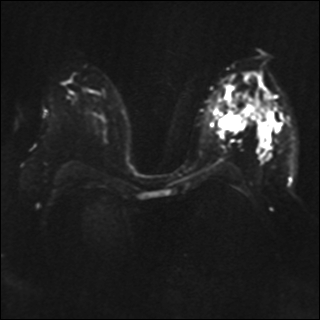
Breast MRI, one axial slice. Position 22 of 41 along the scan axis. Diffusion-weighted series; image 2 of 4 stored at this slice position (different b-values; order by instance number). 1.5 T. 4 mm slice thickness. 320 × 320 image matrix, field of view 340 × 340 mm. Female patient.
Outlined on this slice (outlined manually by an expert reader):
- tumour on diffusion-weighted imaging: box from (x=219, y=114) to (x=249, y=131) px